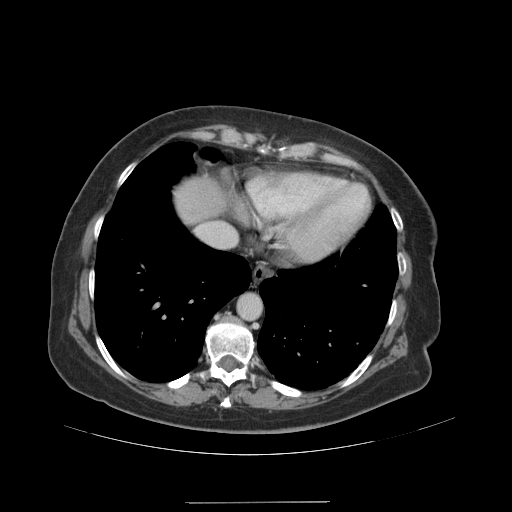
Contrast-enhanced abdominal CT (liver protocol), one axial slice; position 88 of 99 along the scan axis; reconstruction kernel STANDARD; soft-tissue window (W 400 / L 40 HU); 512 × 512 image matrix. Case-level facts recorded for this patient, not image findings: diagnosis: hepatocellular carcinoma (patient treated with transarterial chemoembolisation; whether this scan precedes or follows treatment is not stated here); TNM stage (as recorded): Stage-IVA; Child-Pugh class: A.
Structures marked on this image (semi-automatically segmented with operator editing):
- abdominal aorta: box from (x=238, y=295) to (x=260, y=319) px
- liver parenchyma outside the tumour (the mass and vessels are separate outlines, so this box may not span the whole liver): (x=176, y=182)–(x=220, y=222)